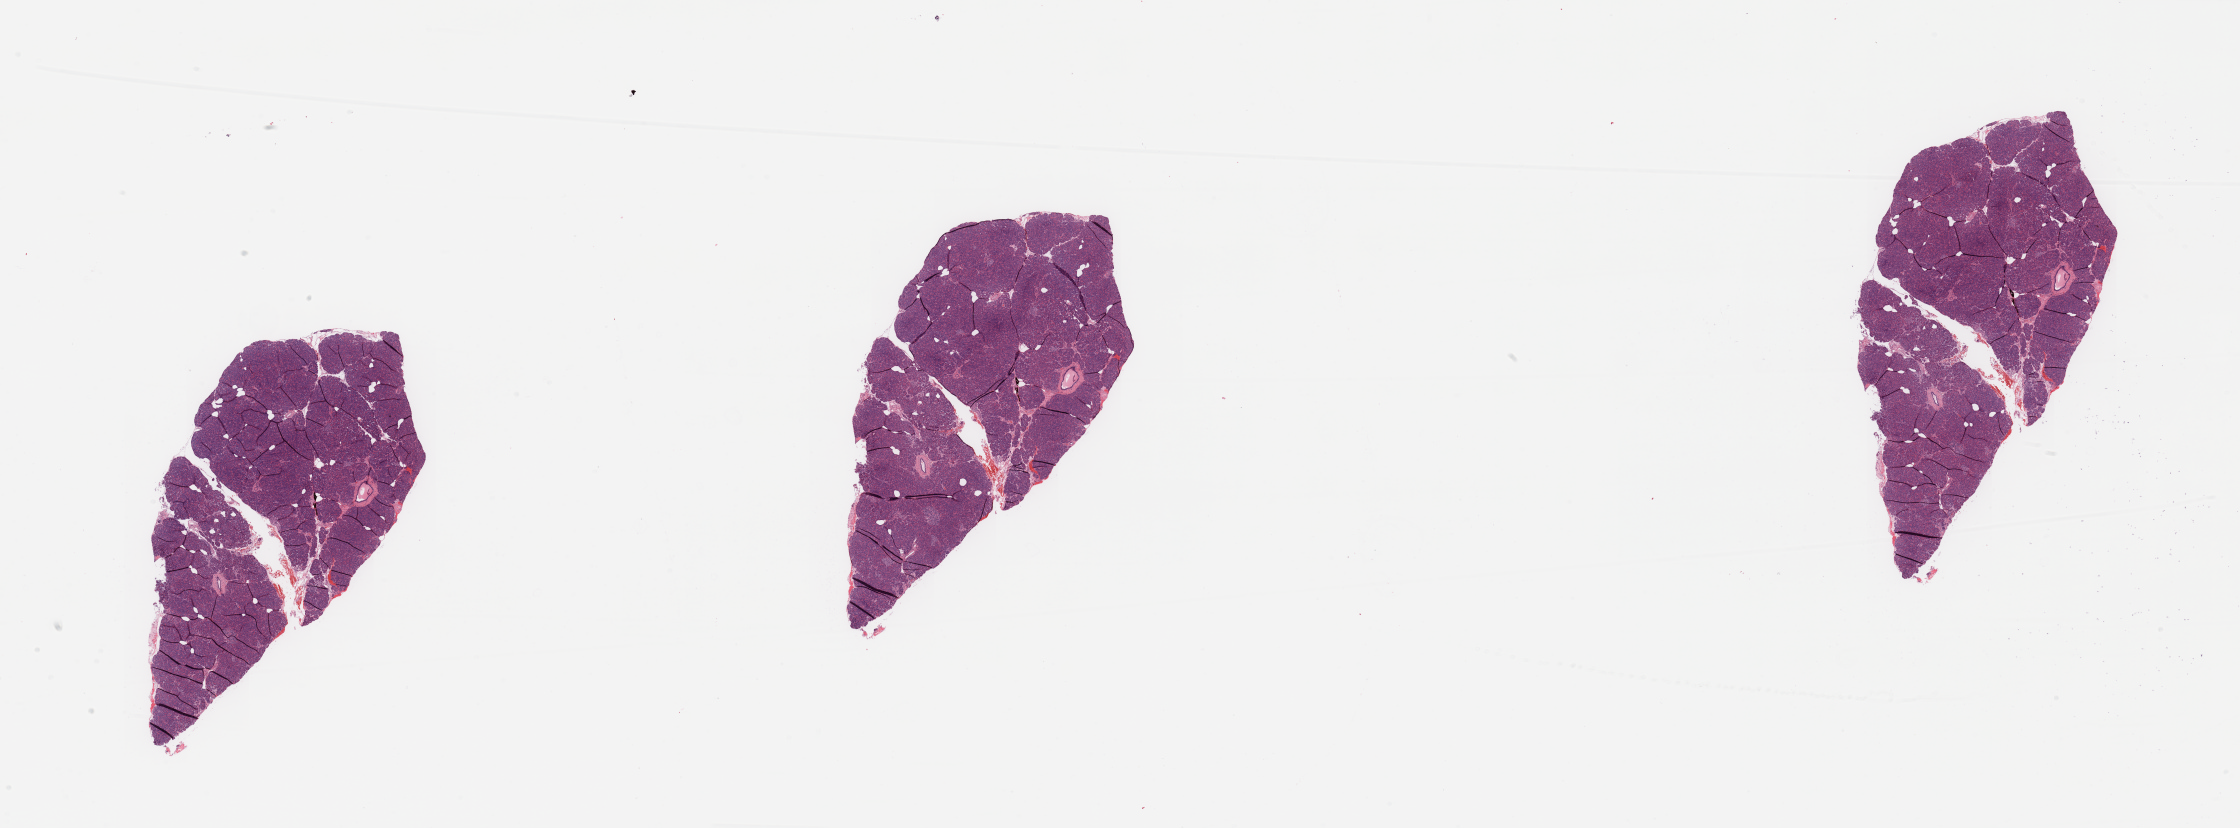
Digitized H&E tissue section (whole slide), low-resolution overview of the scanned area, about 35.4 x 13.1 mm (from a 20x scan); pancreas, normal (non-tumour) tissue. Patient: female, age 67 years.
This section: normal (non-tumour) tissue from the same patient. Patient diagnosis: Infiltrating duct carcinoma, NOS.